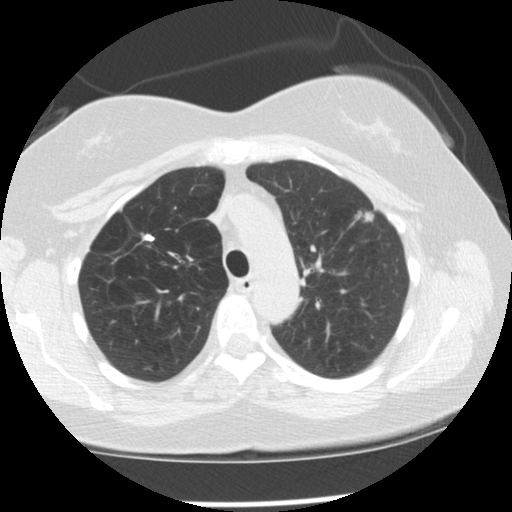
Axial slice from a low-dose chest CT screening exam, second annual screen, lung window (W 1500 / L -600 HU), 2.5 mm slice thickness, slice 36 of 128 in the series, 512 × 512 image matrix. Female, age 57 years at enrolment. Former smoker at enrolment.
Expert-annotated lung lesion, box from (x=349, y=203) to (x=388, y=238) px. Screening reader's record for this exam (one nodule recorded; not confirmed to be the boxed lesion): non-calcified nodule or mass ≥4 mm, left upper lobe, 11 × 7 mm, spiculated (stellate) margins, soft tissue attenuation, pre-existing on the prior screen: yes; interval growth: yes. Official screen result: positive, change unspecified: nodule(s) >= 4 mm or enlarging nodule(s), mass(es), or other non-specific abnormalities suspicious for lung cancer. Later outcome: lung cancer diagnosed 50 days after this screen — adenocarcinoma, NOS, left upper lobe, moderately differentiated (G2), stage IA (AJCC 6th edition), 18 mm at pathology.